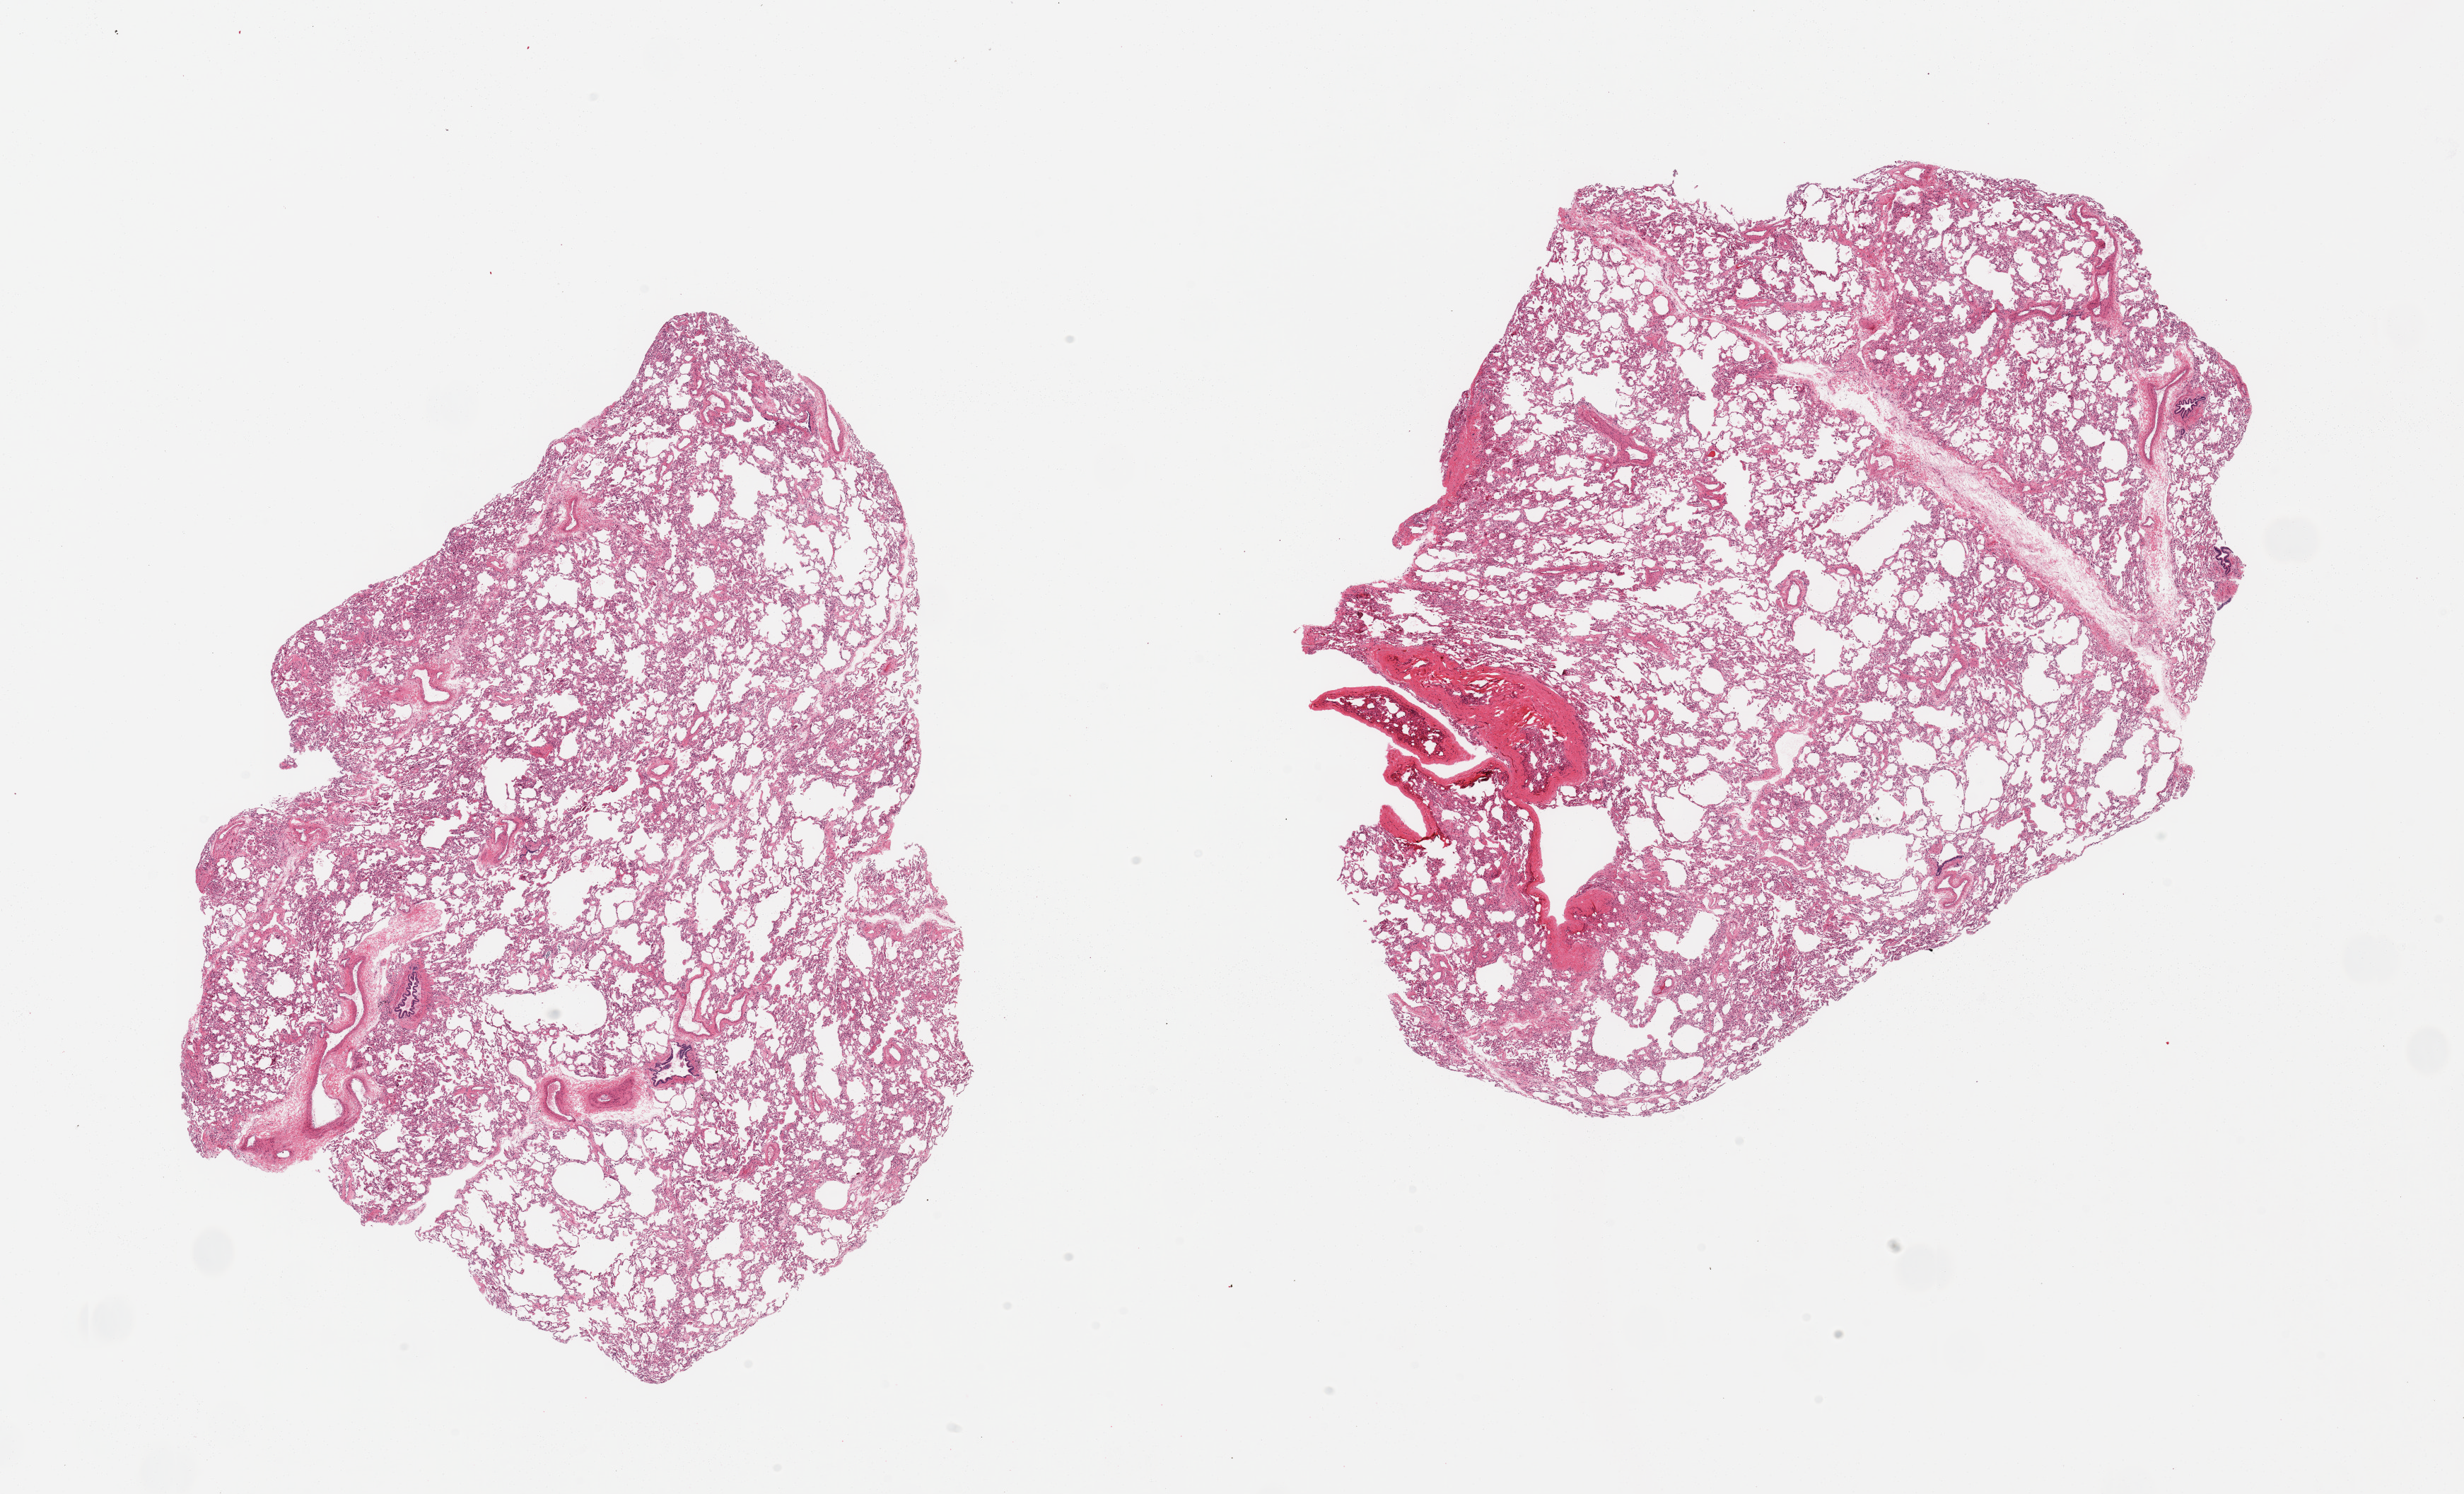
H&E whole-slide image, whole scanned area (about 27.6 x 16.7 mm) shown as a low-resolution overview; PAXgene-fixed, paraffin-embedded tissue; section of lung (target tissue); donor tissue sample. Donor sex: male.
Review note (as recorded): 2 pieces.